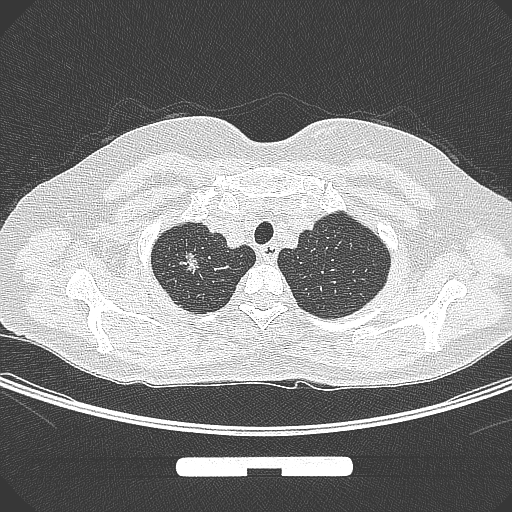
Chest CT, one axial slice; slice 259 of 295 in the series (ordered by position); lung window (W 1500 / L -600 HU); 1 mm slice thickness; 512 × 512 image matrix. Patient: female, 58 years. Case-level facts recorded for this patient, not image findings: clinical TNM (as recorded): T1b N0 M0; histopathological grade: G2-3.
Outlined on this slice (bounding box drawn by a radiologist):
- lung tumour (recorded histology: adenocarcinoma): box from (x=173, y=245) to (x=207, y=284) px